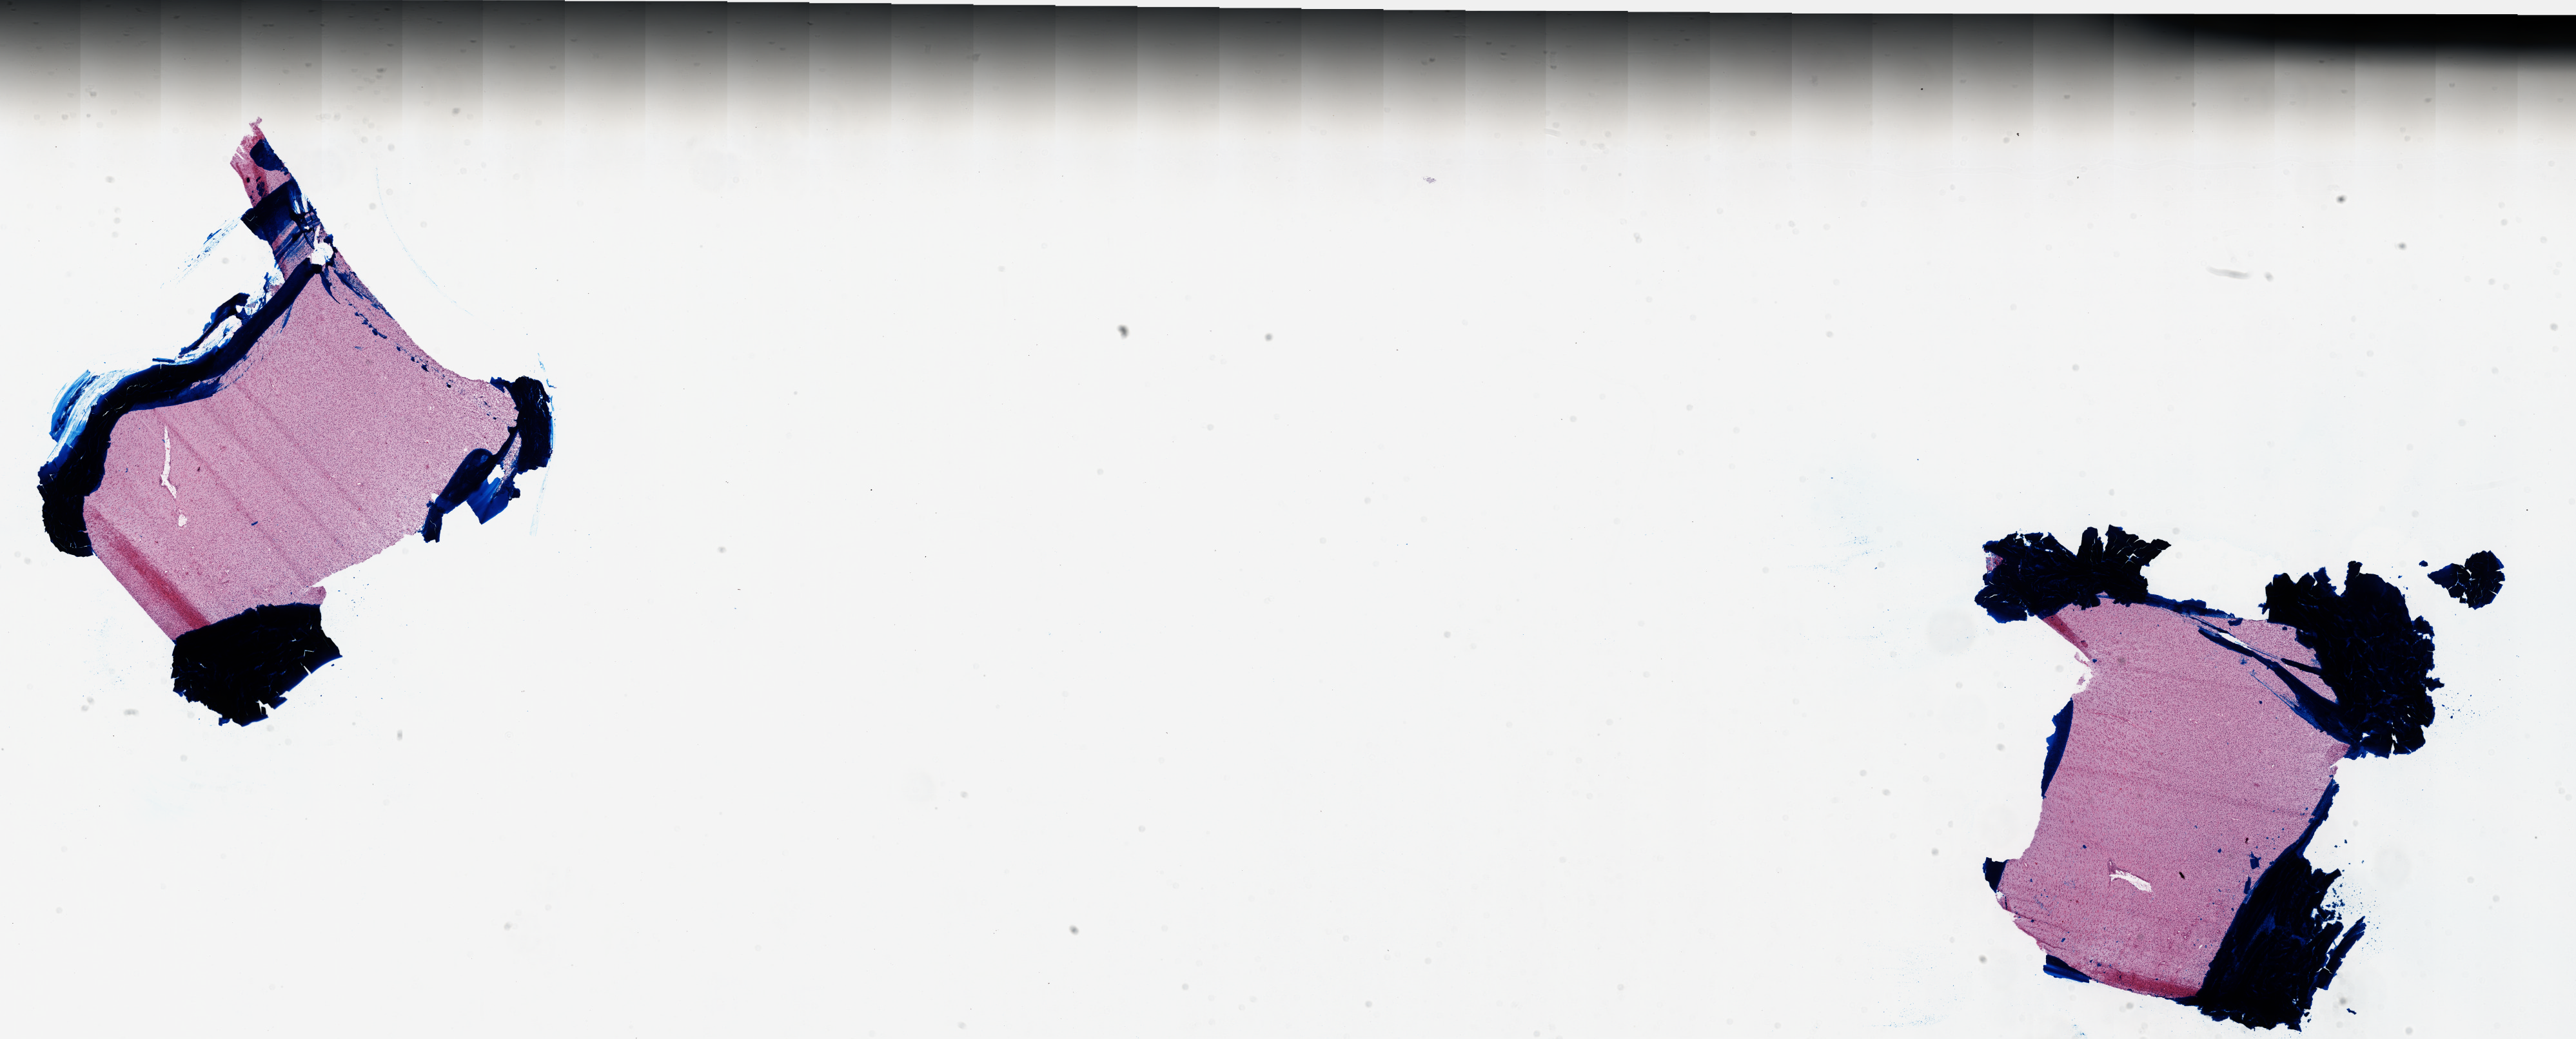
H&E whole-slide image — whole scanned area (about 32.0 x 12.9 mm, acquisition: 20x scan) shown as a low-resolution overview, frozen section from the top of the tissue portion, brain, primary tumour sample. Patient: male, age at initial diagnosis 73 years. Slide review estimates, as recorded: tumour cells 80%, tumour nuclei 95%, normal cells 0%, stromal cells 20%, necrosis 0%.
Pathologic diagnosis: Glioblastoma.